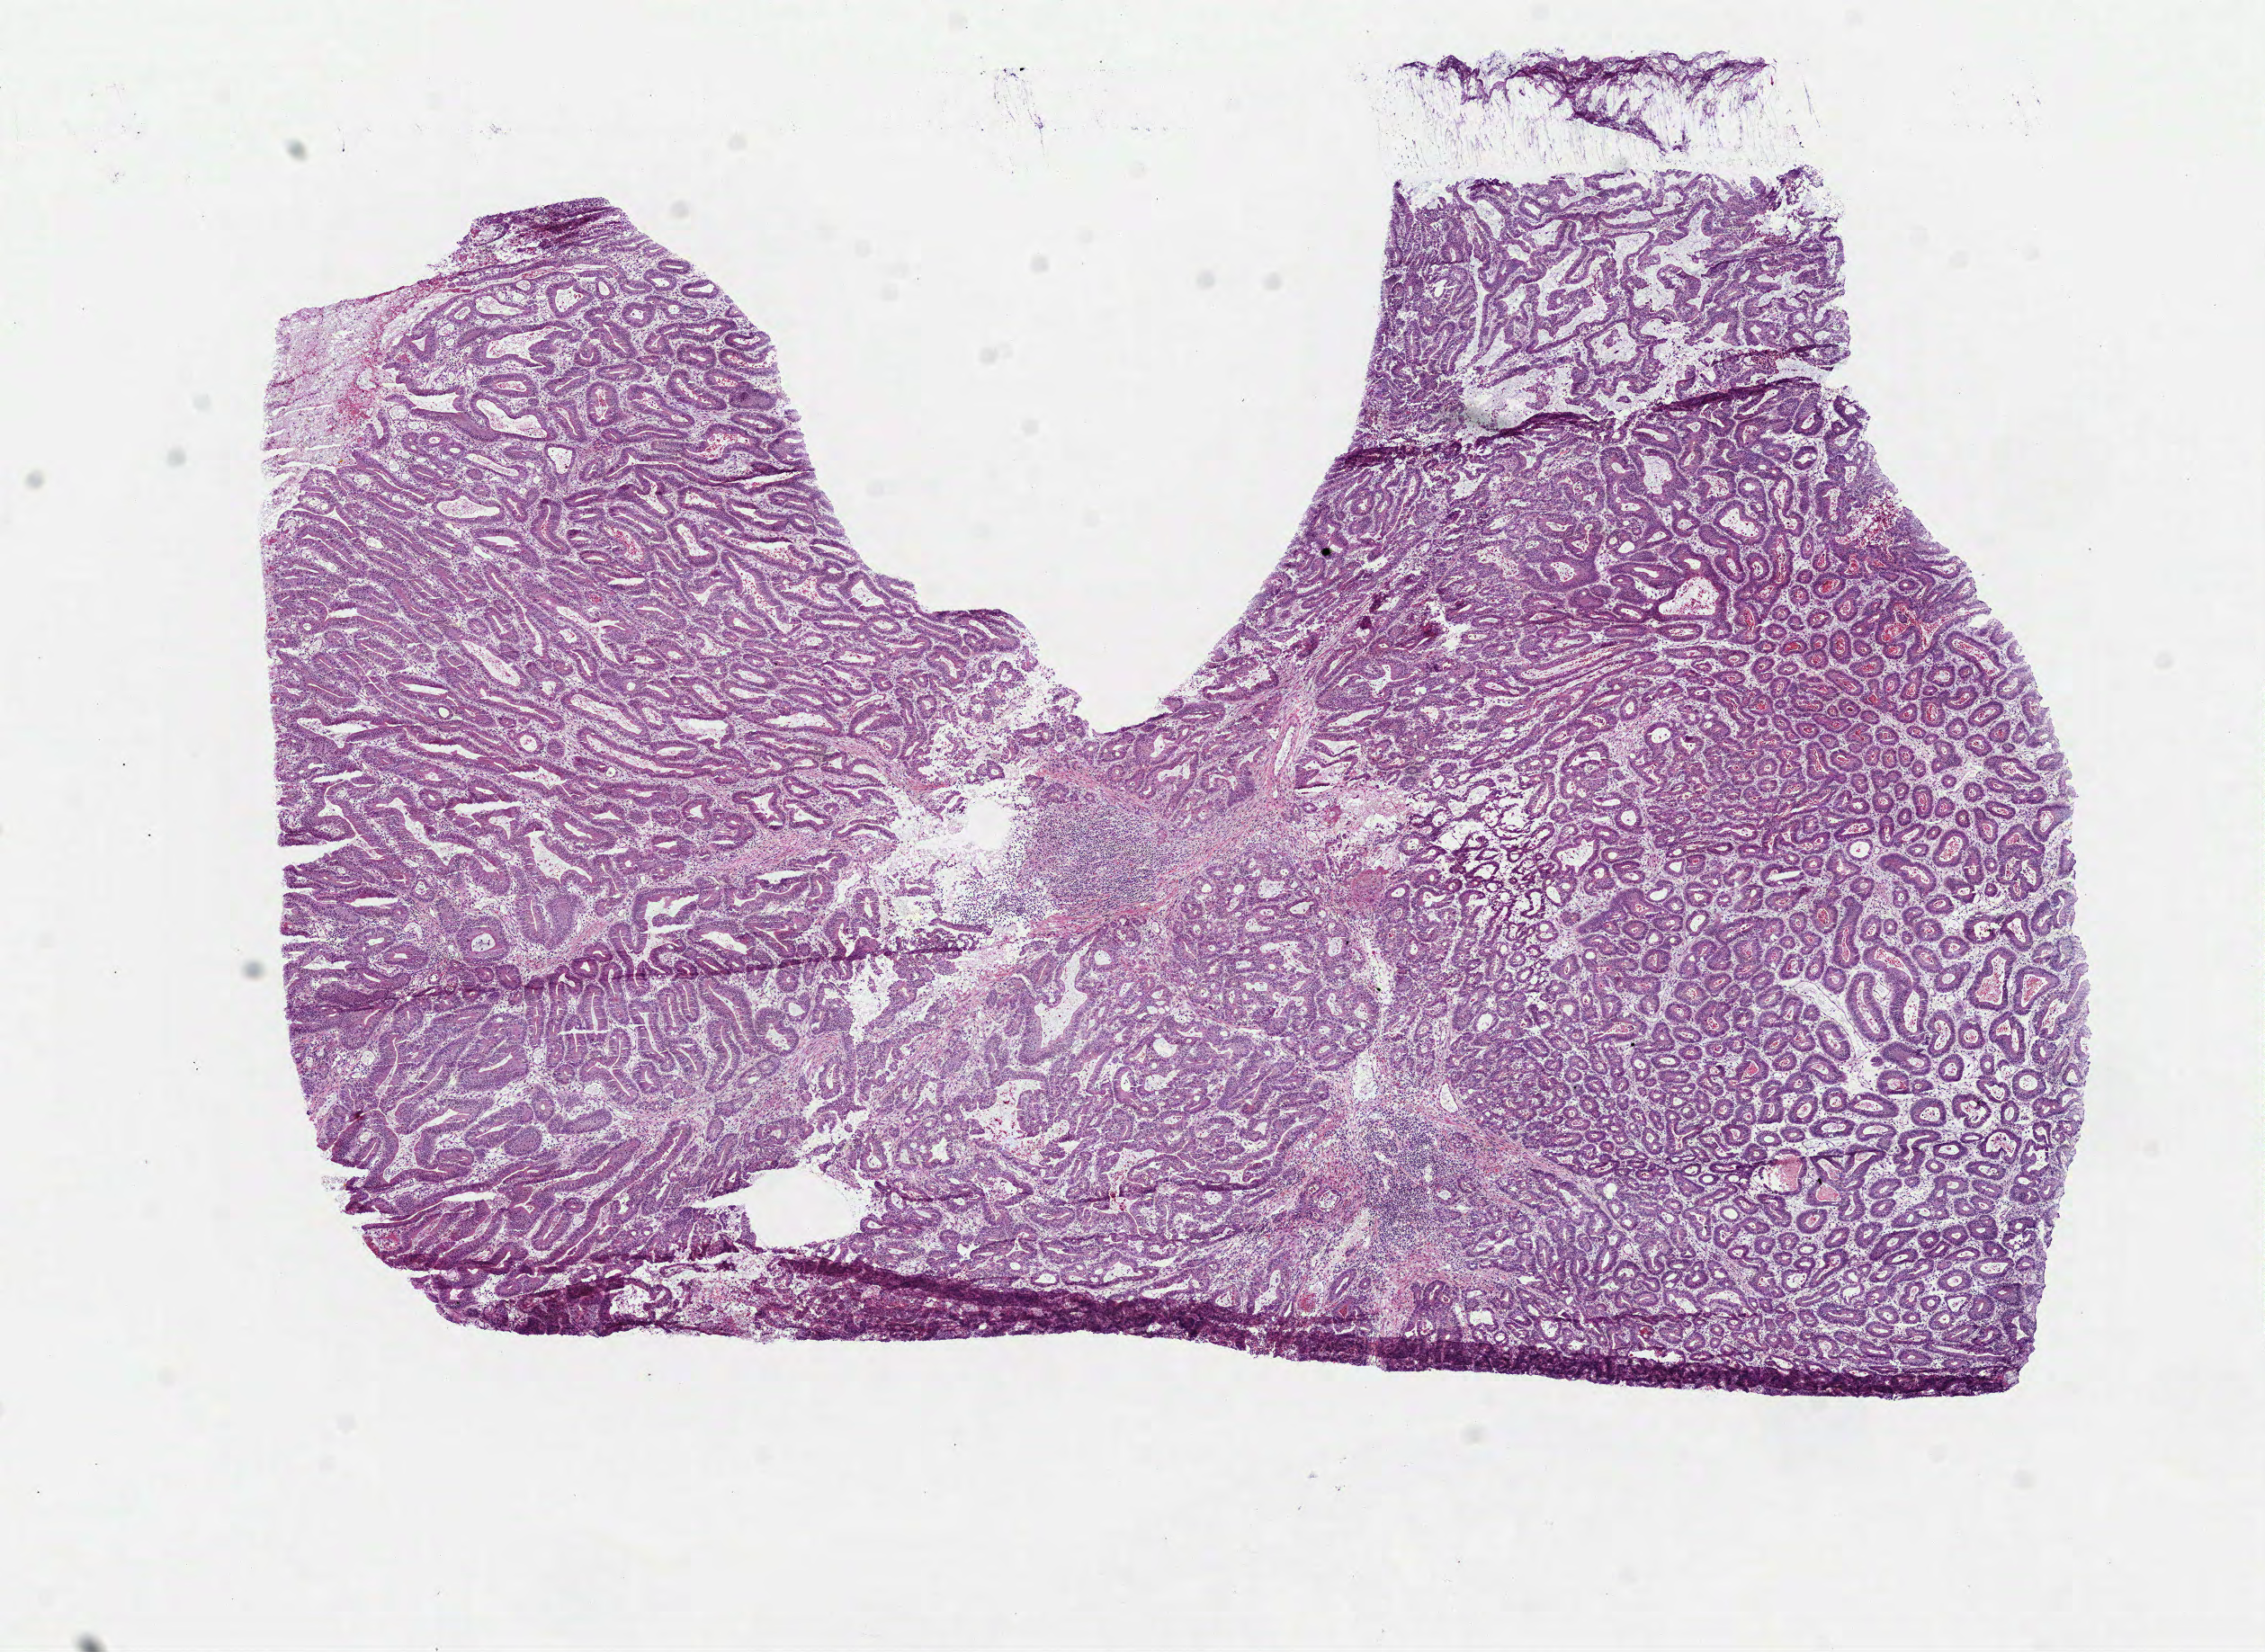
Digitized Hematoxylin and eosin (H&E) stained tissue section (whole slide), low-resolution overview of the scanned area, about 10.2 x 7.4 mm (from a 40x scan), frozen section, primary tumour sample from the colon. Patient: male, age at initial diagnosis 60 years. Pathologist review of this section (percent, as recorded): tumour cells 88%, tumour nuclei 80%, normal cells 0%, stromal cells 12%, necrosis 0%.
- AJCC pathologic stage: IIA (7th edition)
- histologic diagnosis: Adenocarcinoma, NOS